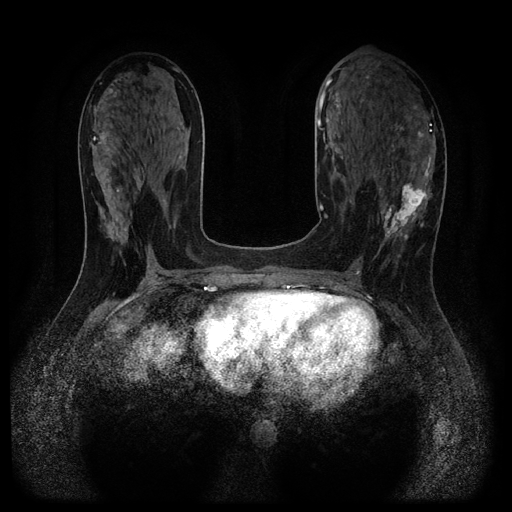
Breast MRI (dynamic contrast-enhanced, multi-phase), one axial slice. Dynamic contrast-enhanced series, time point 2 of 5 at this slice position (early post-contrast). 1.5 T. TE 2.7 ms, TR 5.4 ms. 512 × 512 image matrix, field of view 330 × 330 mm. Female patient, age 43 years.
Outlined on this slice (semi-automatic segmentation, software-assisted and operator-edited):
- breast lesion (labelled 'tumour' in the annotation; benign lesions carry a separate 'benign' label): bounding box (x1, y1, x2, y2) in pixels: (376, 180, 432, 256)